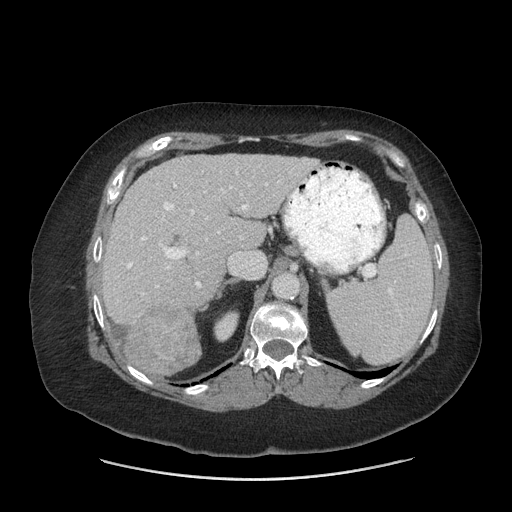
Contrast-enhanced abdominal CT (liver protocol), one axial slice; position 44 of 69 along the scan axis; reconstruction kernel STANDARD; 140 kVp; soft-tissue window (W 400 / L 40 HU); 2.5 mm slice thickness; 512 × 512 image matrix, field of view 420 × 420 mm. From the clinical record (not read from this slice): diagnosis: hepatocellular carcinoma (patient treated with transarterial chemoembolisation; whether this scan precedes or follows treatment is not stated here); TNM stage (as recorded): Stage-IIIB; Child-Pugh class: A; tumour nodularity: multinodular.
Annotated regions visible in this slice (semi-automatically segmented with operator editing):
- liver parenchyma outside the tumour (the mass and vessels are separate outlines, so this box may not span the whole liver): box from (x=102, y=154) to (x=317, y=351) px
- mass: (x=126, y=300)–(x=201, y=374)
- liver vessels: (x=126, y=172)–(x=279, y=295)